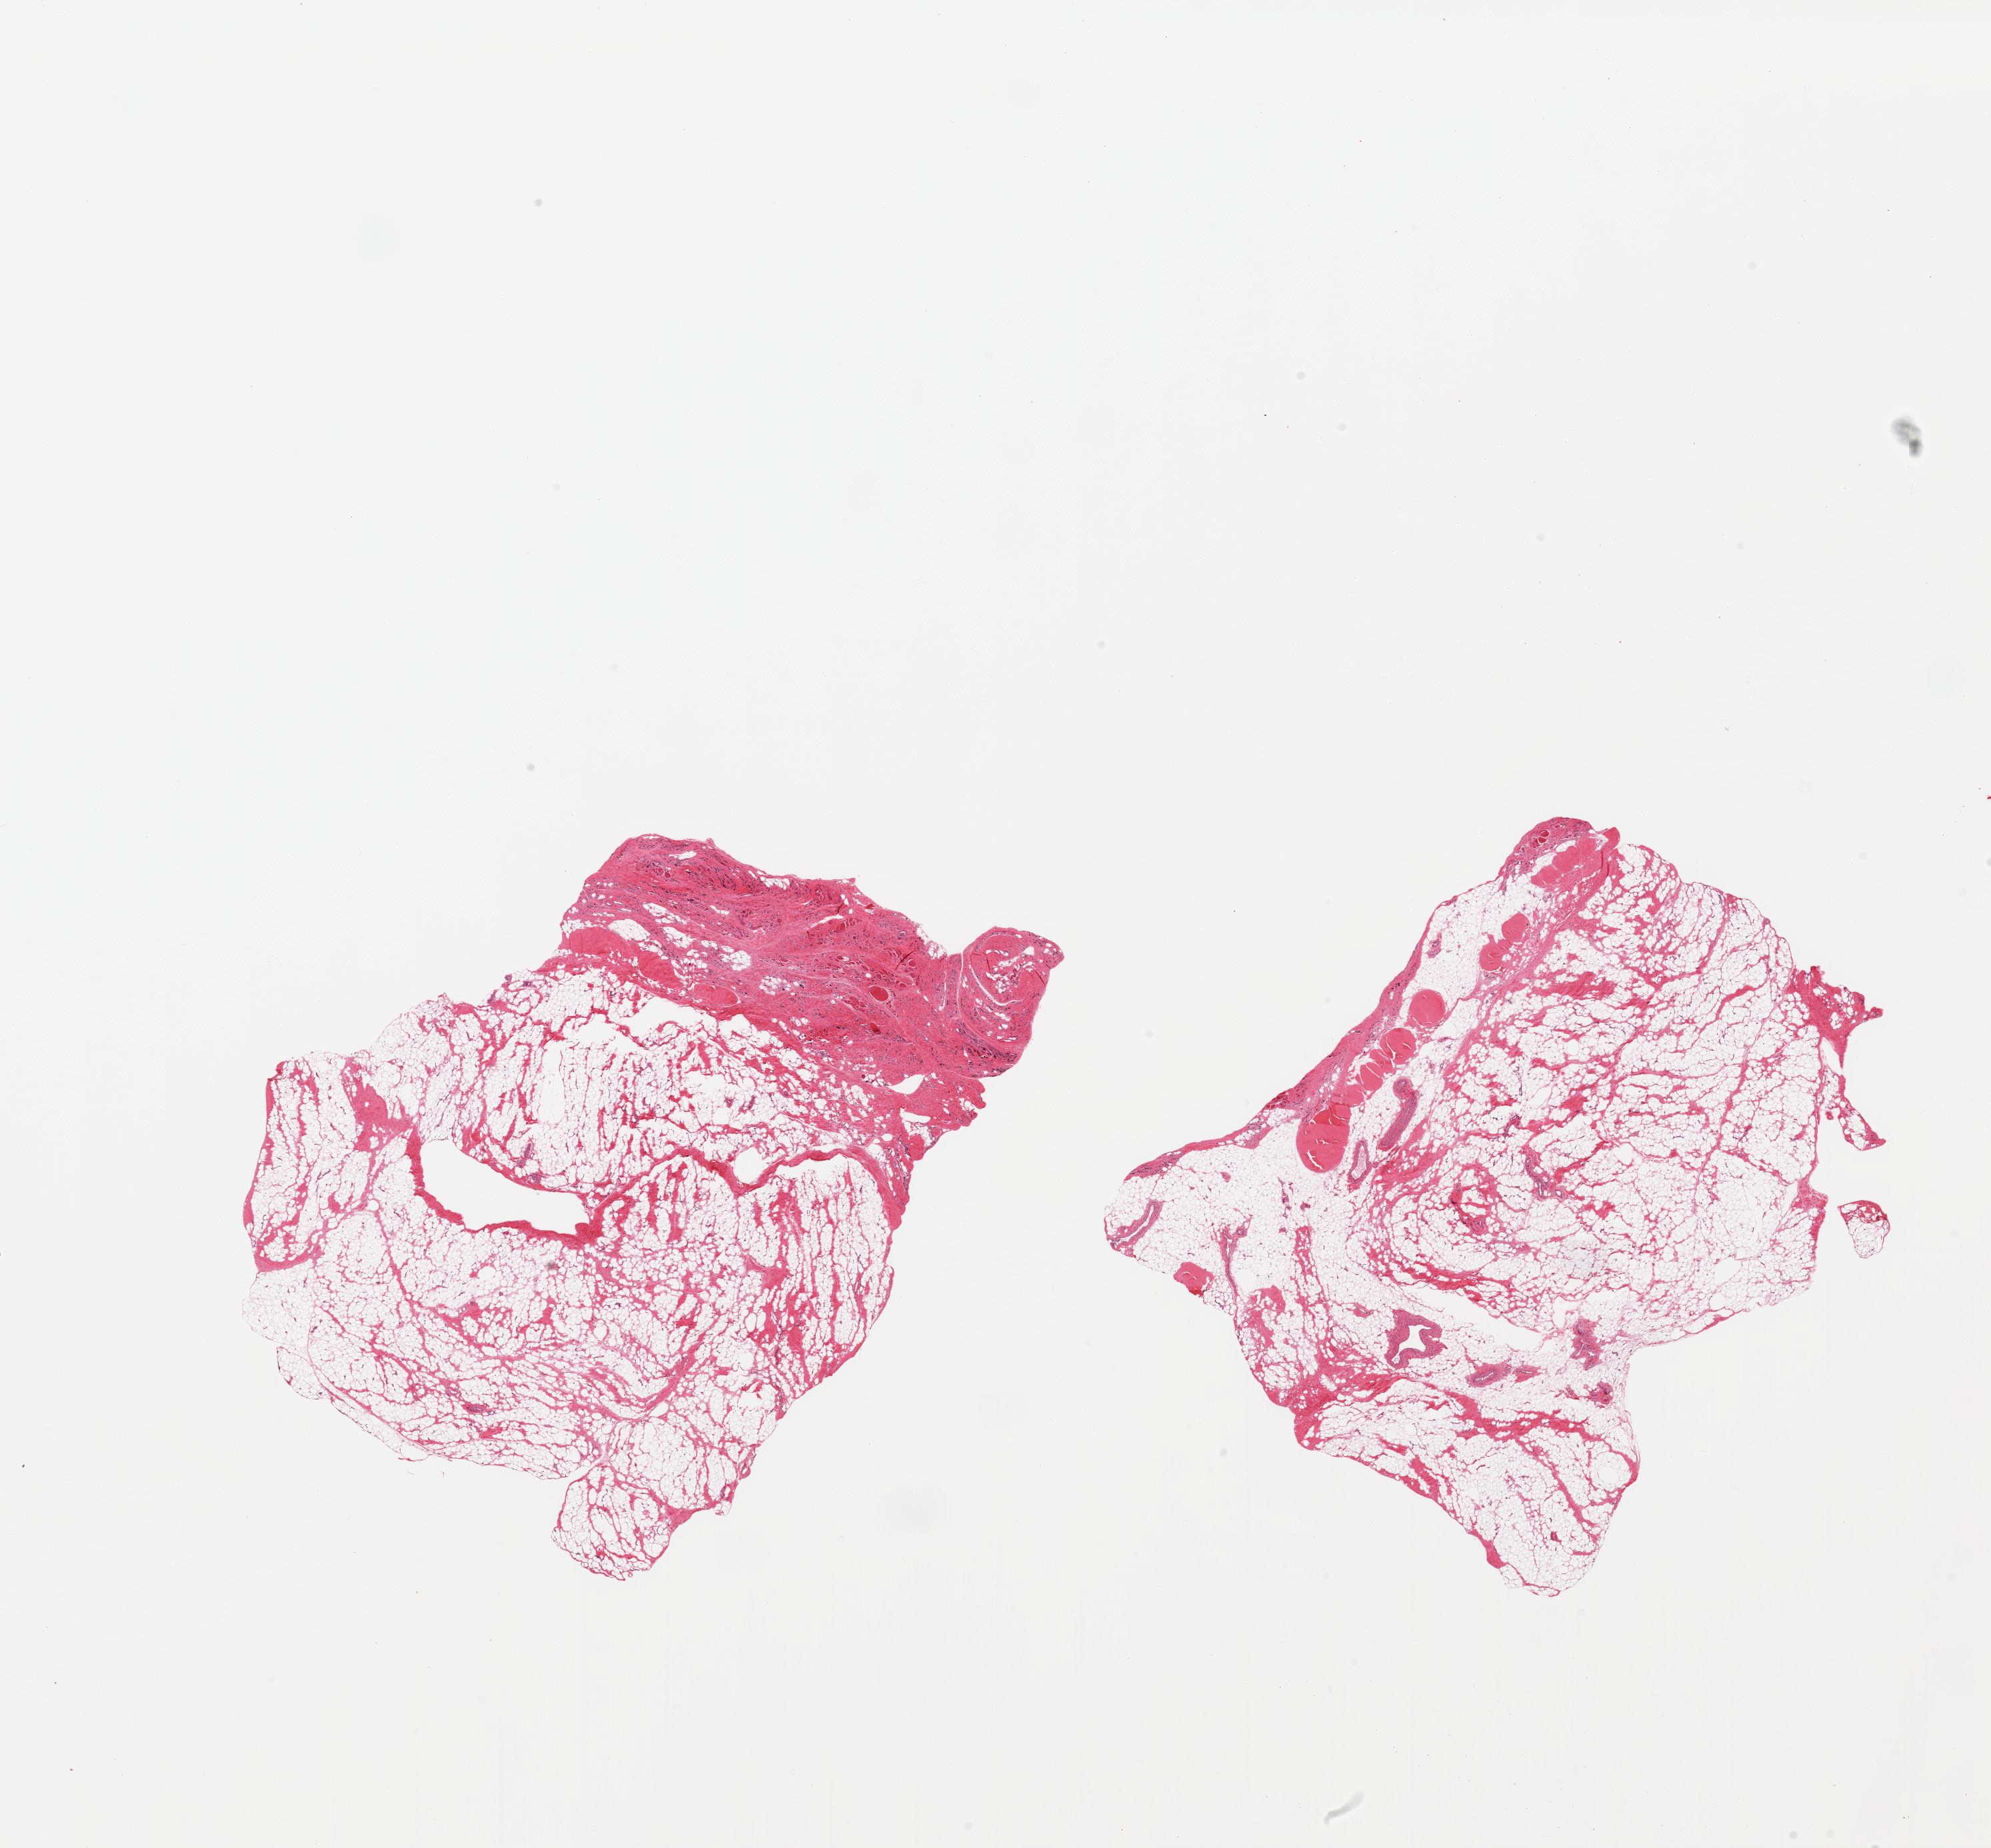
Digitized haematoxylin and eosin-stained section — whole scanned area (about 23.6 x 21.9 mm, acquisition: 20x scan) shown as a low-resolution overview, PAXgene-fixed paraffin-embedded (PFPE) section, sampled site (target tissue): skeletal muscle, tissue donor sample. Donor: female.
Pathologist's review note for this sample: 2 pieces, minimal muscle, mainly fibroadipose tissue.